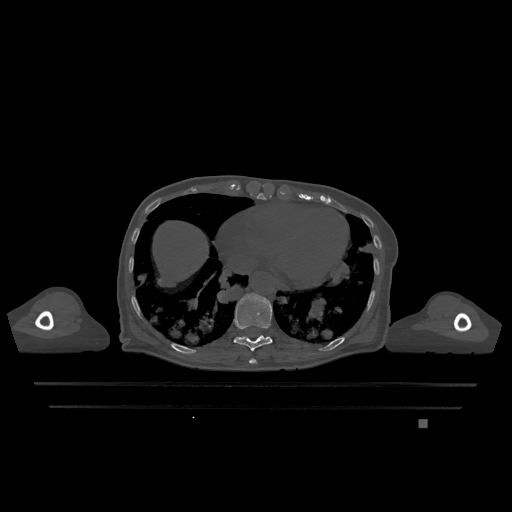
CT including the spine, one axial slice. Slice 637 of 1317 in the series (ordered by position). Bone window (W 1800 / L 400 HU). 0.5 mm slice thickness. 512 × 512 image matrix, field of view 500 × 500 mm. Female patient, age 74 years. Case-level facts recorded for this patient, not image findings: primary cancer: lung; vertebrae with lytic lesions (as recorded): T1, T4, T5, T6, L4, L5.
Outlined on this slice (semi-automatic segmentation, software-assisted and operator-edited):
- T10 vertebra: bounding box (x1, y1, x2, y2) in pixels: (234, 293, 273, 351)
- T9 vertebra: (249, 358, 257, 364)